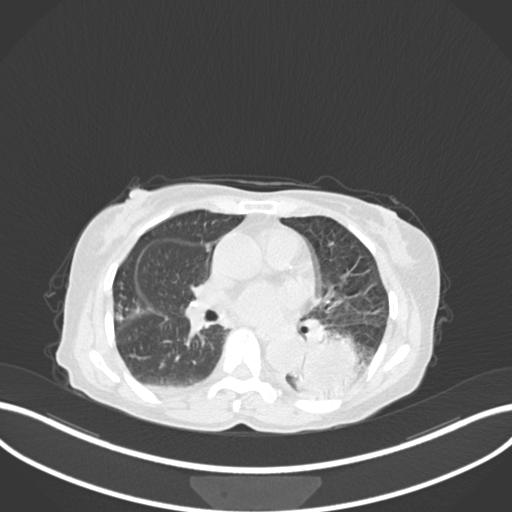
Chest CT, one axial slice. Position 81 of 233 along the scan axis. Reconstruction kernel B30f. Lung window (W 1500 / L -600 HU). 512 × 512 image matrix, field of view 400 × 400 mm. Female patient, age 78 years. From the clinical record (not read from this slice): clinical TNM (as recorded): T3 N0 M1.
Structures marked on this image (bounding box drawn by a radiologist):
- lung tumour (recorded histology: squamous cell carcinoma): bounding box [x1, y1, x2, y2] px = [290, 328, 364, 398]